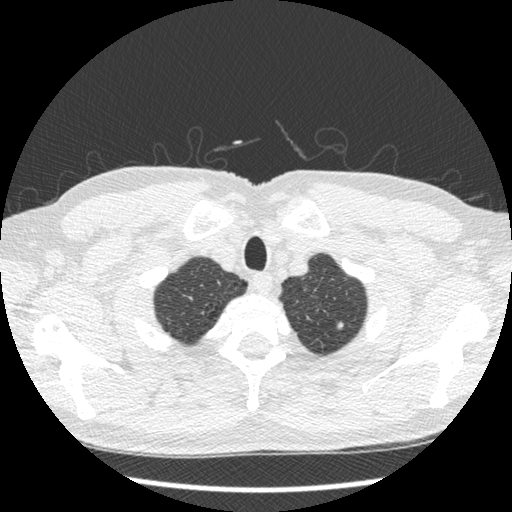
Low-dose screening chest CT, one axial slice; slice 409 of 439 in the series (ordered by position); reconstruction kernel STANDARD; lung window (W 1500 / L -600 HU); 1.25 mm slice thickness; 512 × 512 image matrix, field of view 340 × 340 mm.
Outlined on this slice (outlined manually by an expert reader):
- lesion 1 (nodule, upper lobe of left lung): bounding box <337,321,344,329> (left, top, right, bottom; pixels)